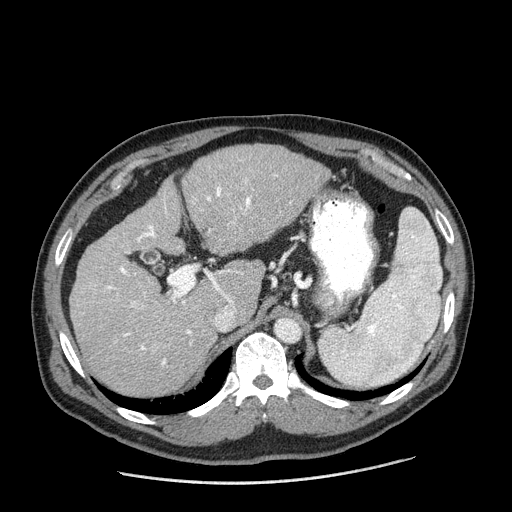
Contrast-enhanced abdominal CT (liver protocol), one axial slice; position 123 of 198 along the scan axis; reconstruction kernel STANDARD; one of 2 acquisitions stored at this slice position; soft-tissue window (W 400 / L 40 HU); 2.5 mm slice thickness; 512 × 512 image matrix, field of view 400 × 400 mm. From the clinical record (not read from this slice): diagnosis: hepatocellular carcinoma (patient treated with transarterial chemoembolisation; whether this scan precedes or follows treatment is not stated here); TNM stage (as recorded): Stage-II; Child-Pugh class: A; tumour differentiation: moderately differentiated.
Annotated regions visible in this slice (semi-automatically segmented with operator editing):
- liver parenchyma outside the tumour (the mass and vessels are separate outlines, so this box may not span the whole liver): bounding box (x1, y1, x2, y2) in pixels: (69, 144, 330, 396)
- liver vessels: (106, 175, 276, 366)